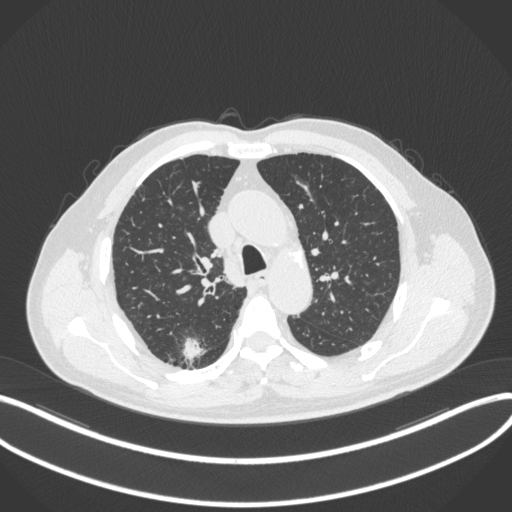
Chest CT, one axial slice; slice 262 of 366 in the series (ordered by position); 120 kVp; lung window (W 1500 / L -600 HU); 512 × 512 image matrix, field of view 400 × 400 mm. Patient: male, 69 years. From the clinical record (not read from this slice): clinical TNM (as recorded): T1b N0 M0; histopathological grade: G2-3.
Structures marked on this image (bounding box drawn by a radiologist):
- lung tumour (recorded histology: adenocarcinoma): bounding box [x1, y1, x2, y2] px = [178, 334, 206, 360]